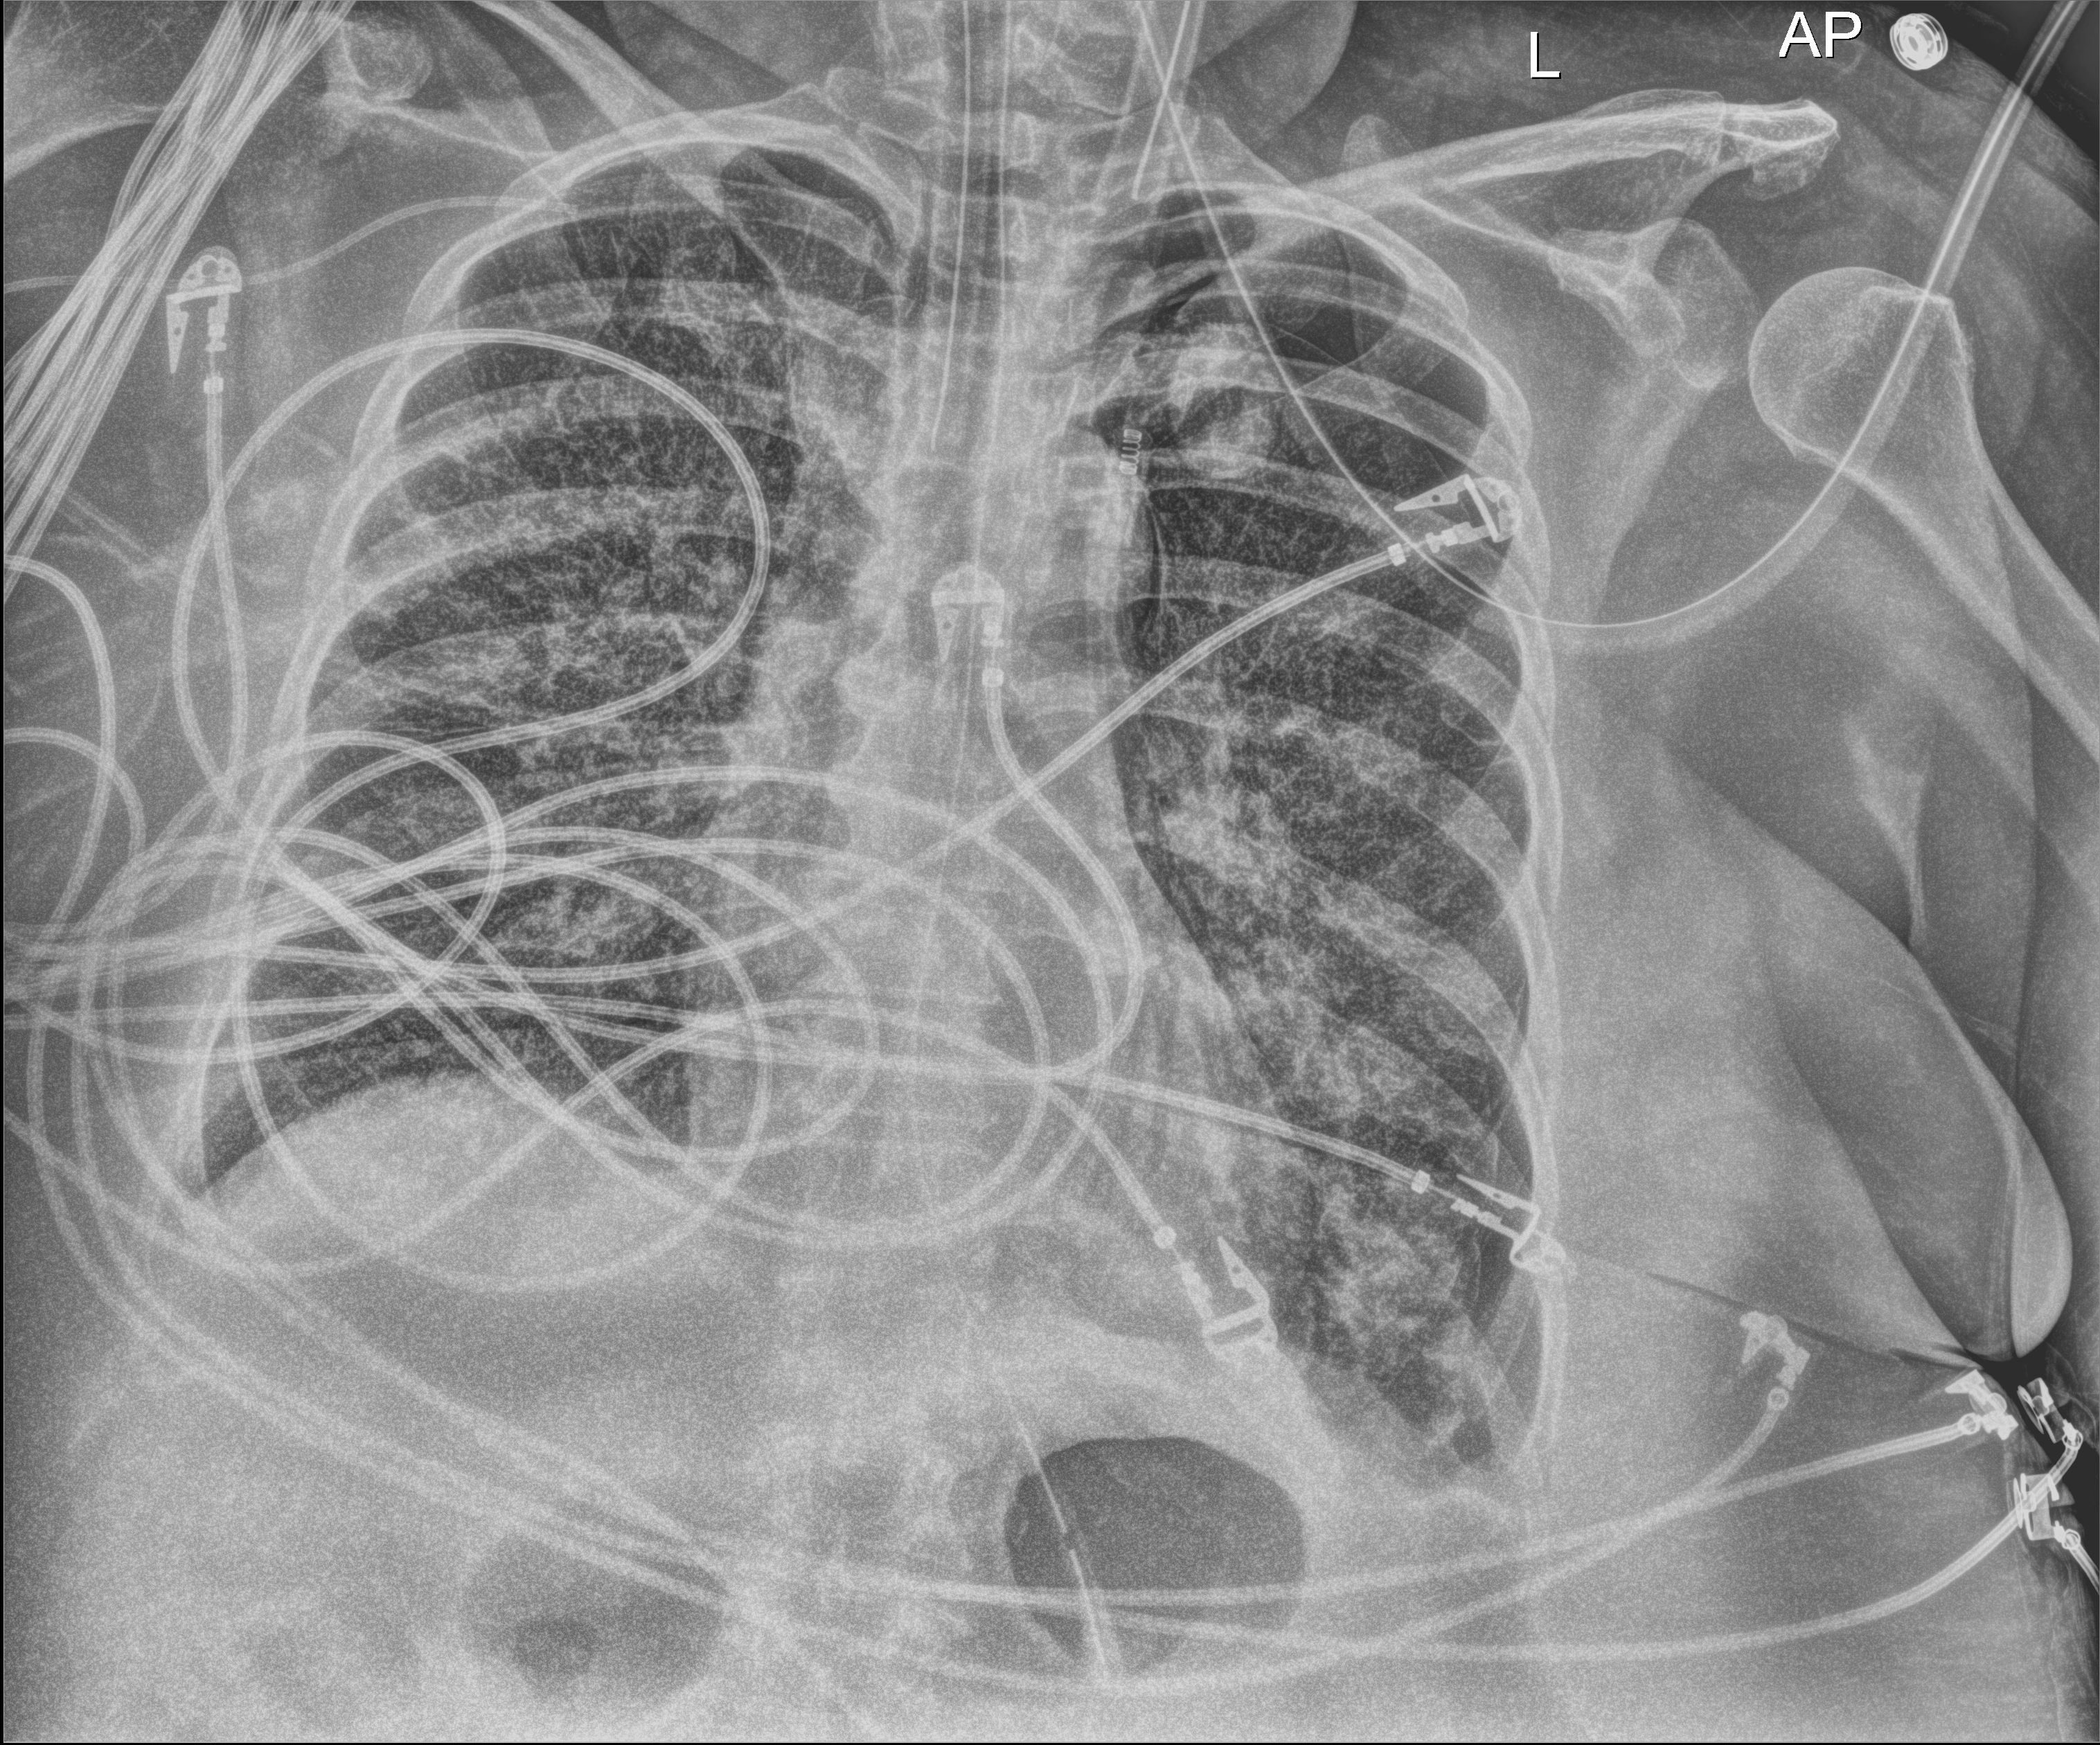
Bedside chest radiograph (digital radiography); anteroposterior (AP) projection. Female patient hospitalised with COVID-19, age 60–74 years.
Hospital-stay facts (about this admission, not read from this image; timing relative to this image not recorded): mechanically ventilated during this hospital stay: yes; chronic kidney disease (admission record): no; admitted to intensive care during this hospital stay: yes.